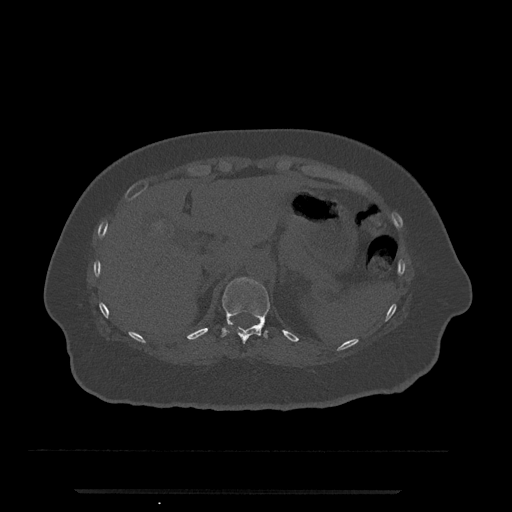
CT including the spine, one axial slice. Position 226 of 797 along the scan axis. Bone window (W 1800 / L 400 HU). 0.5 mm slice thickness. 512 × 512 image matrix, field of view 440 × 440 mm. Patient: female, 51 years. From the clinical record (not read from this slice): primary cancer: neuro; vertebrae with lytic lesions (as recorded): T8.
Outlined on this slice (semi-automatically segmented with operator editing):
- T11 vertebra: box from (x=221, y=277) to (x=270, y=343) px